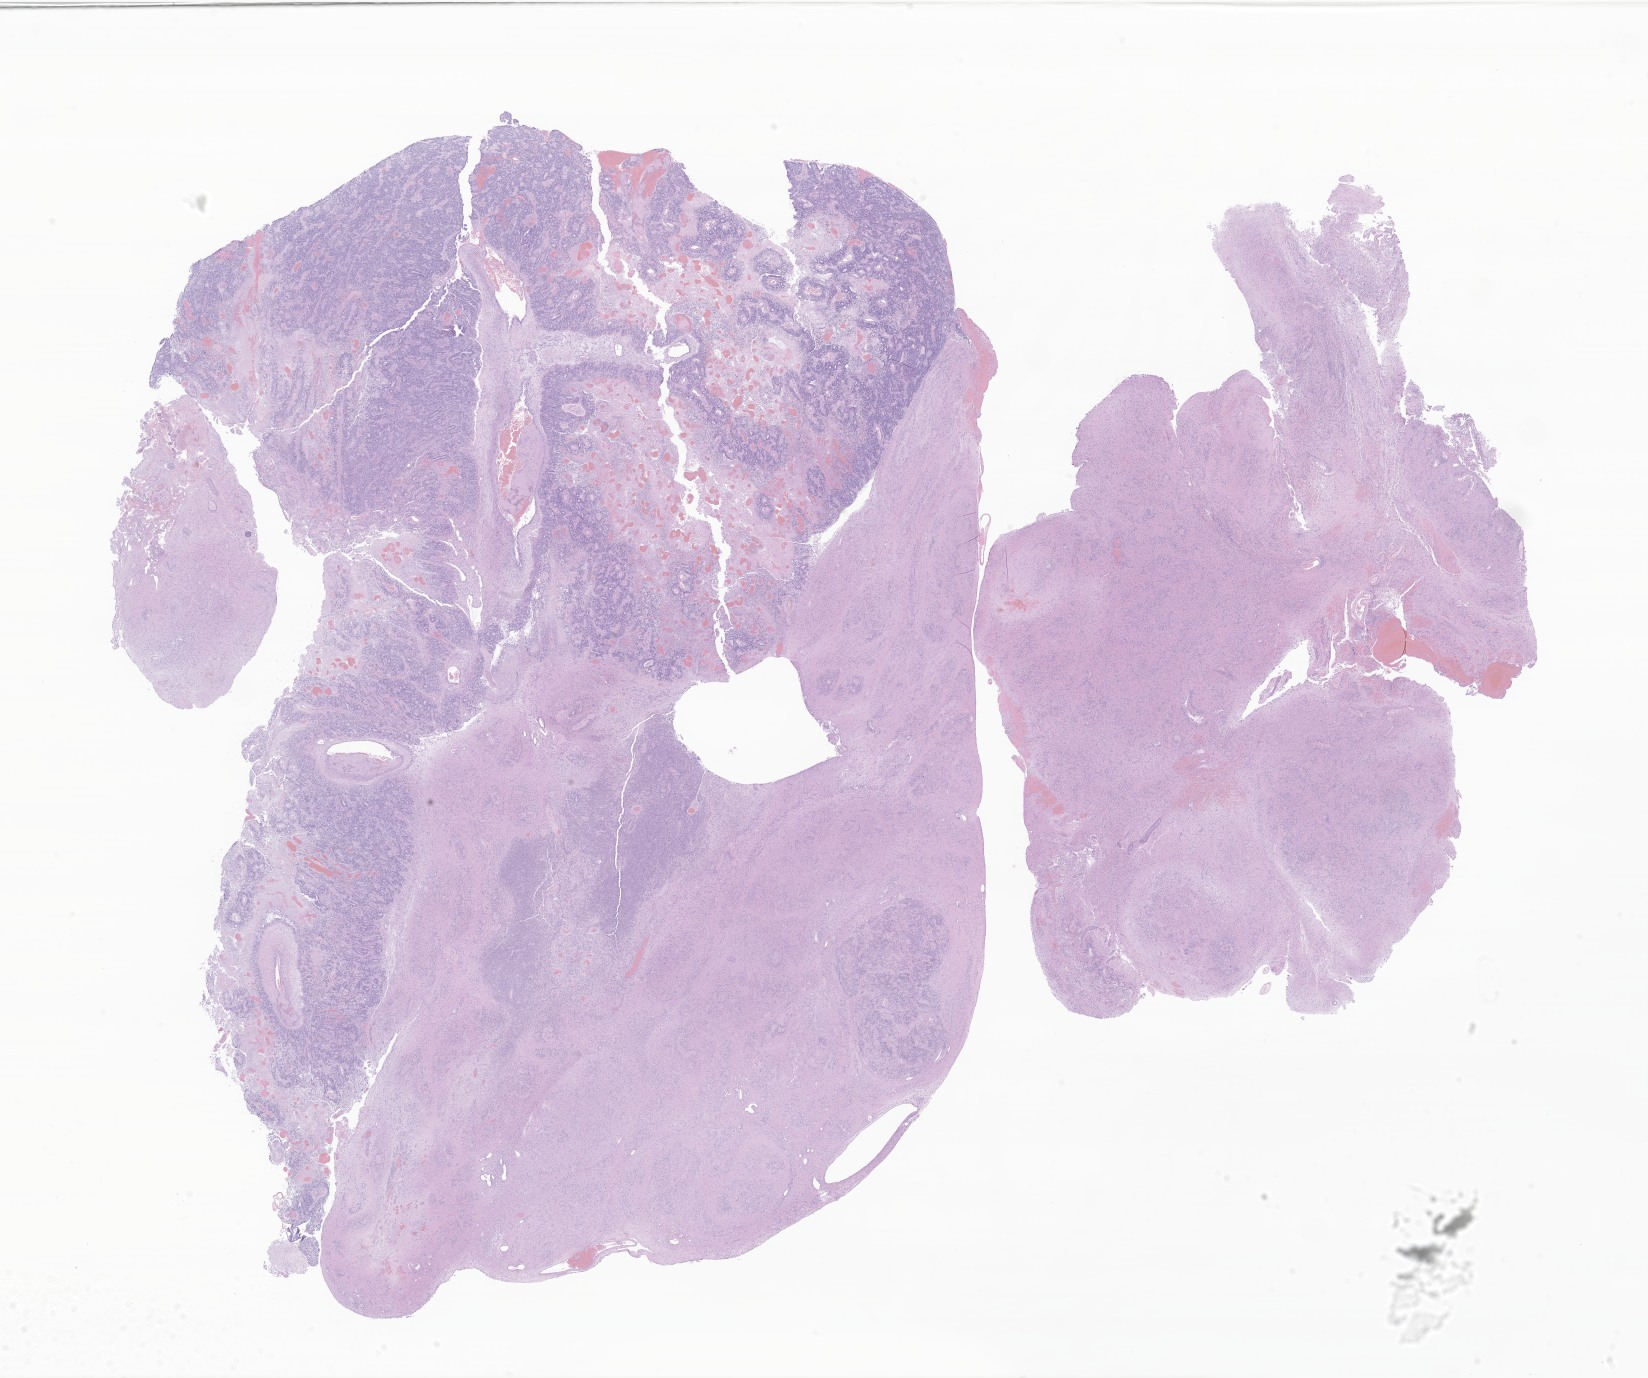
Digitized hematoxylin and eosin (H&E)-stained section of tumor tissue from the cerebral ventricle, shown as a low-resolution overview of the whole scanned area (about 27.8 x 23.2 mm), FFPE section. Patient female; age 95 months.
• recorded diagnosis: Ependymoma, anaplastic